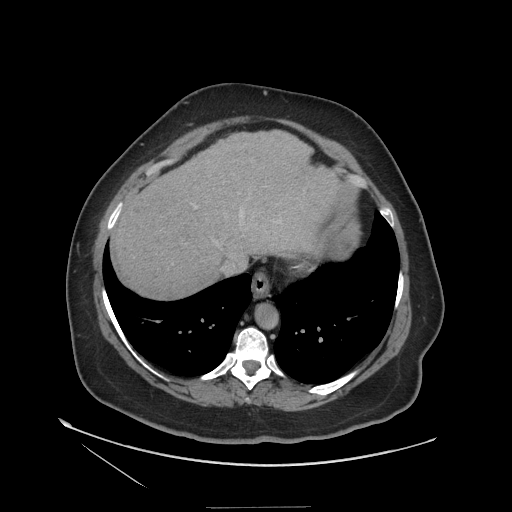
Contrast-enhanced abdominal CT (liver protocol), one axial slice; slice 98 of 127 in the series (ordered by position); 140 kVp; soft-tissue window (W 400 / L 40 HU); 512 × 512 image matrix. From the clinical record (not read from this slice): diagnosis: hepatocellular carcinoma (patient treated with transarterial chemoembolisation; whether this scan precedes or follows treatment is not stated here); TNM stage (as recorded): Stage-II; Child-Pugh class: A; tumour differentiation: well differentiated; tumour nodularity: multinodular.
Structures marked on this image (semi-automatically segmented with operator editing):
- liver parenchyma outside the tumour (the mass and vessels are separate outlines, so this box may not span the whole liver): box from (x=112, y=130) to (x=348, y=296) px
- liver vessels: (x=240, y=211)–(x=243, y=217)